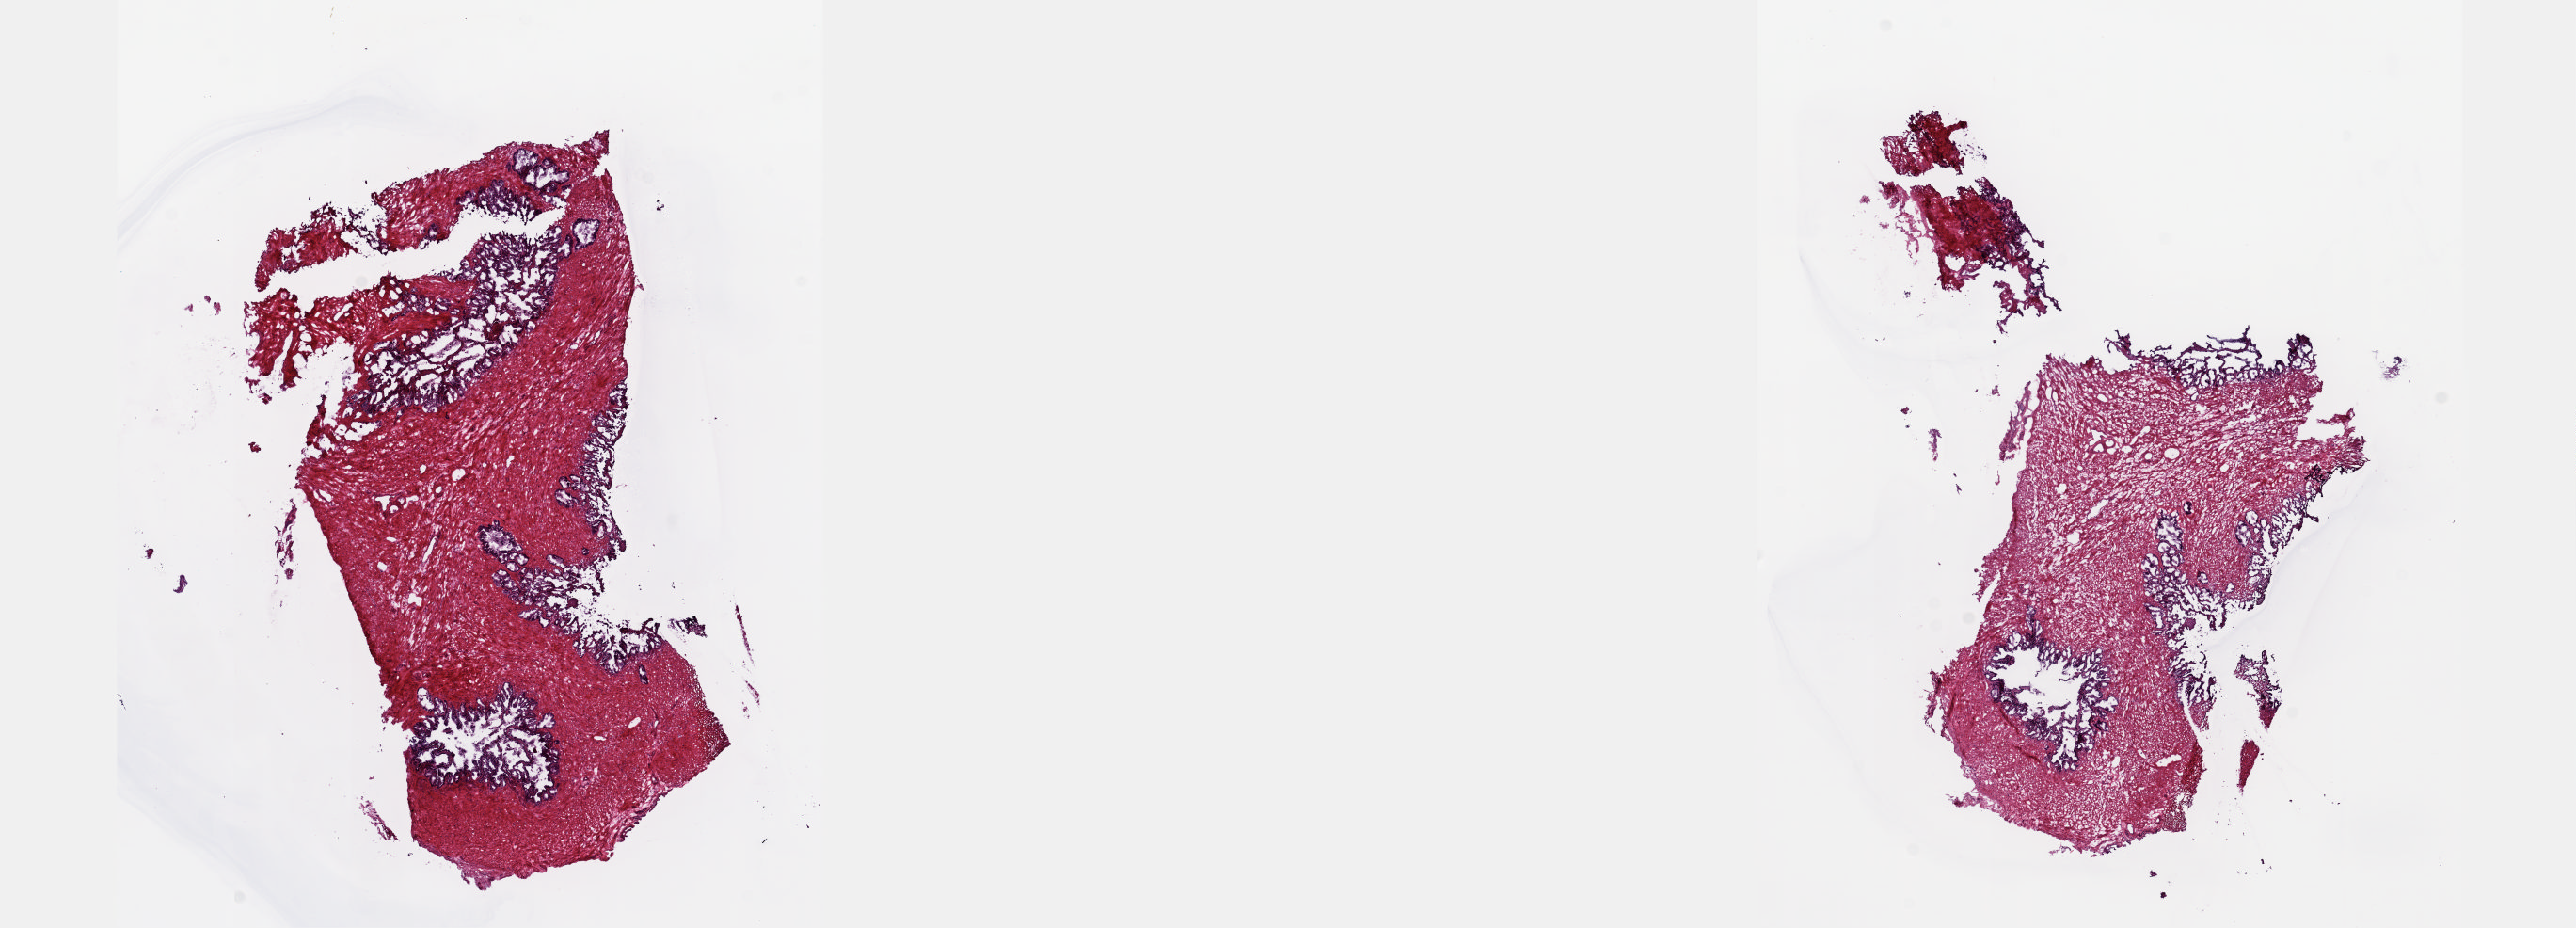
Whole-slide histology image, Hematoxylin and eosin (H&E) stained, low-resolution overview of the scanned area, about 22.1 x 8.0 mm (from a 20x scan). Frozen section. Solid tissue normal (non-tumour tissue) sample from the prostate. Male, age 69 years at initial diagnosis. Slide review estimates, as recorded: tumour cells 0%, tumour nuclei 0%.
This section: solid tissue normal sample (biorepository sample class). Patient diagnosis: Adenocarcinoma, NOS (prostate gland).